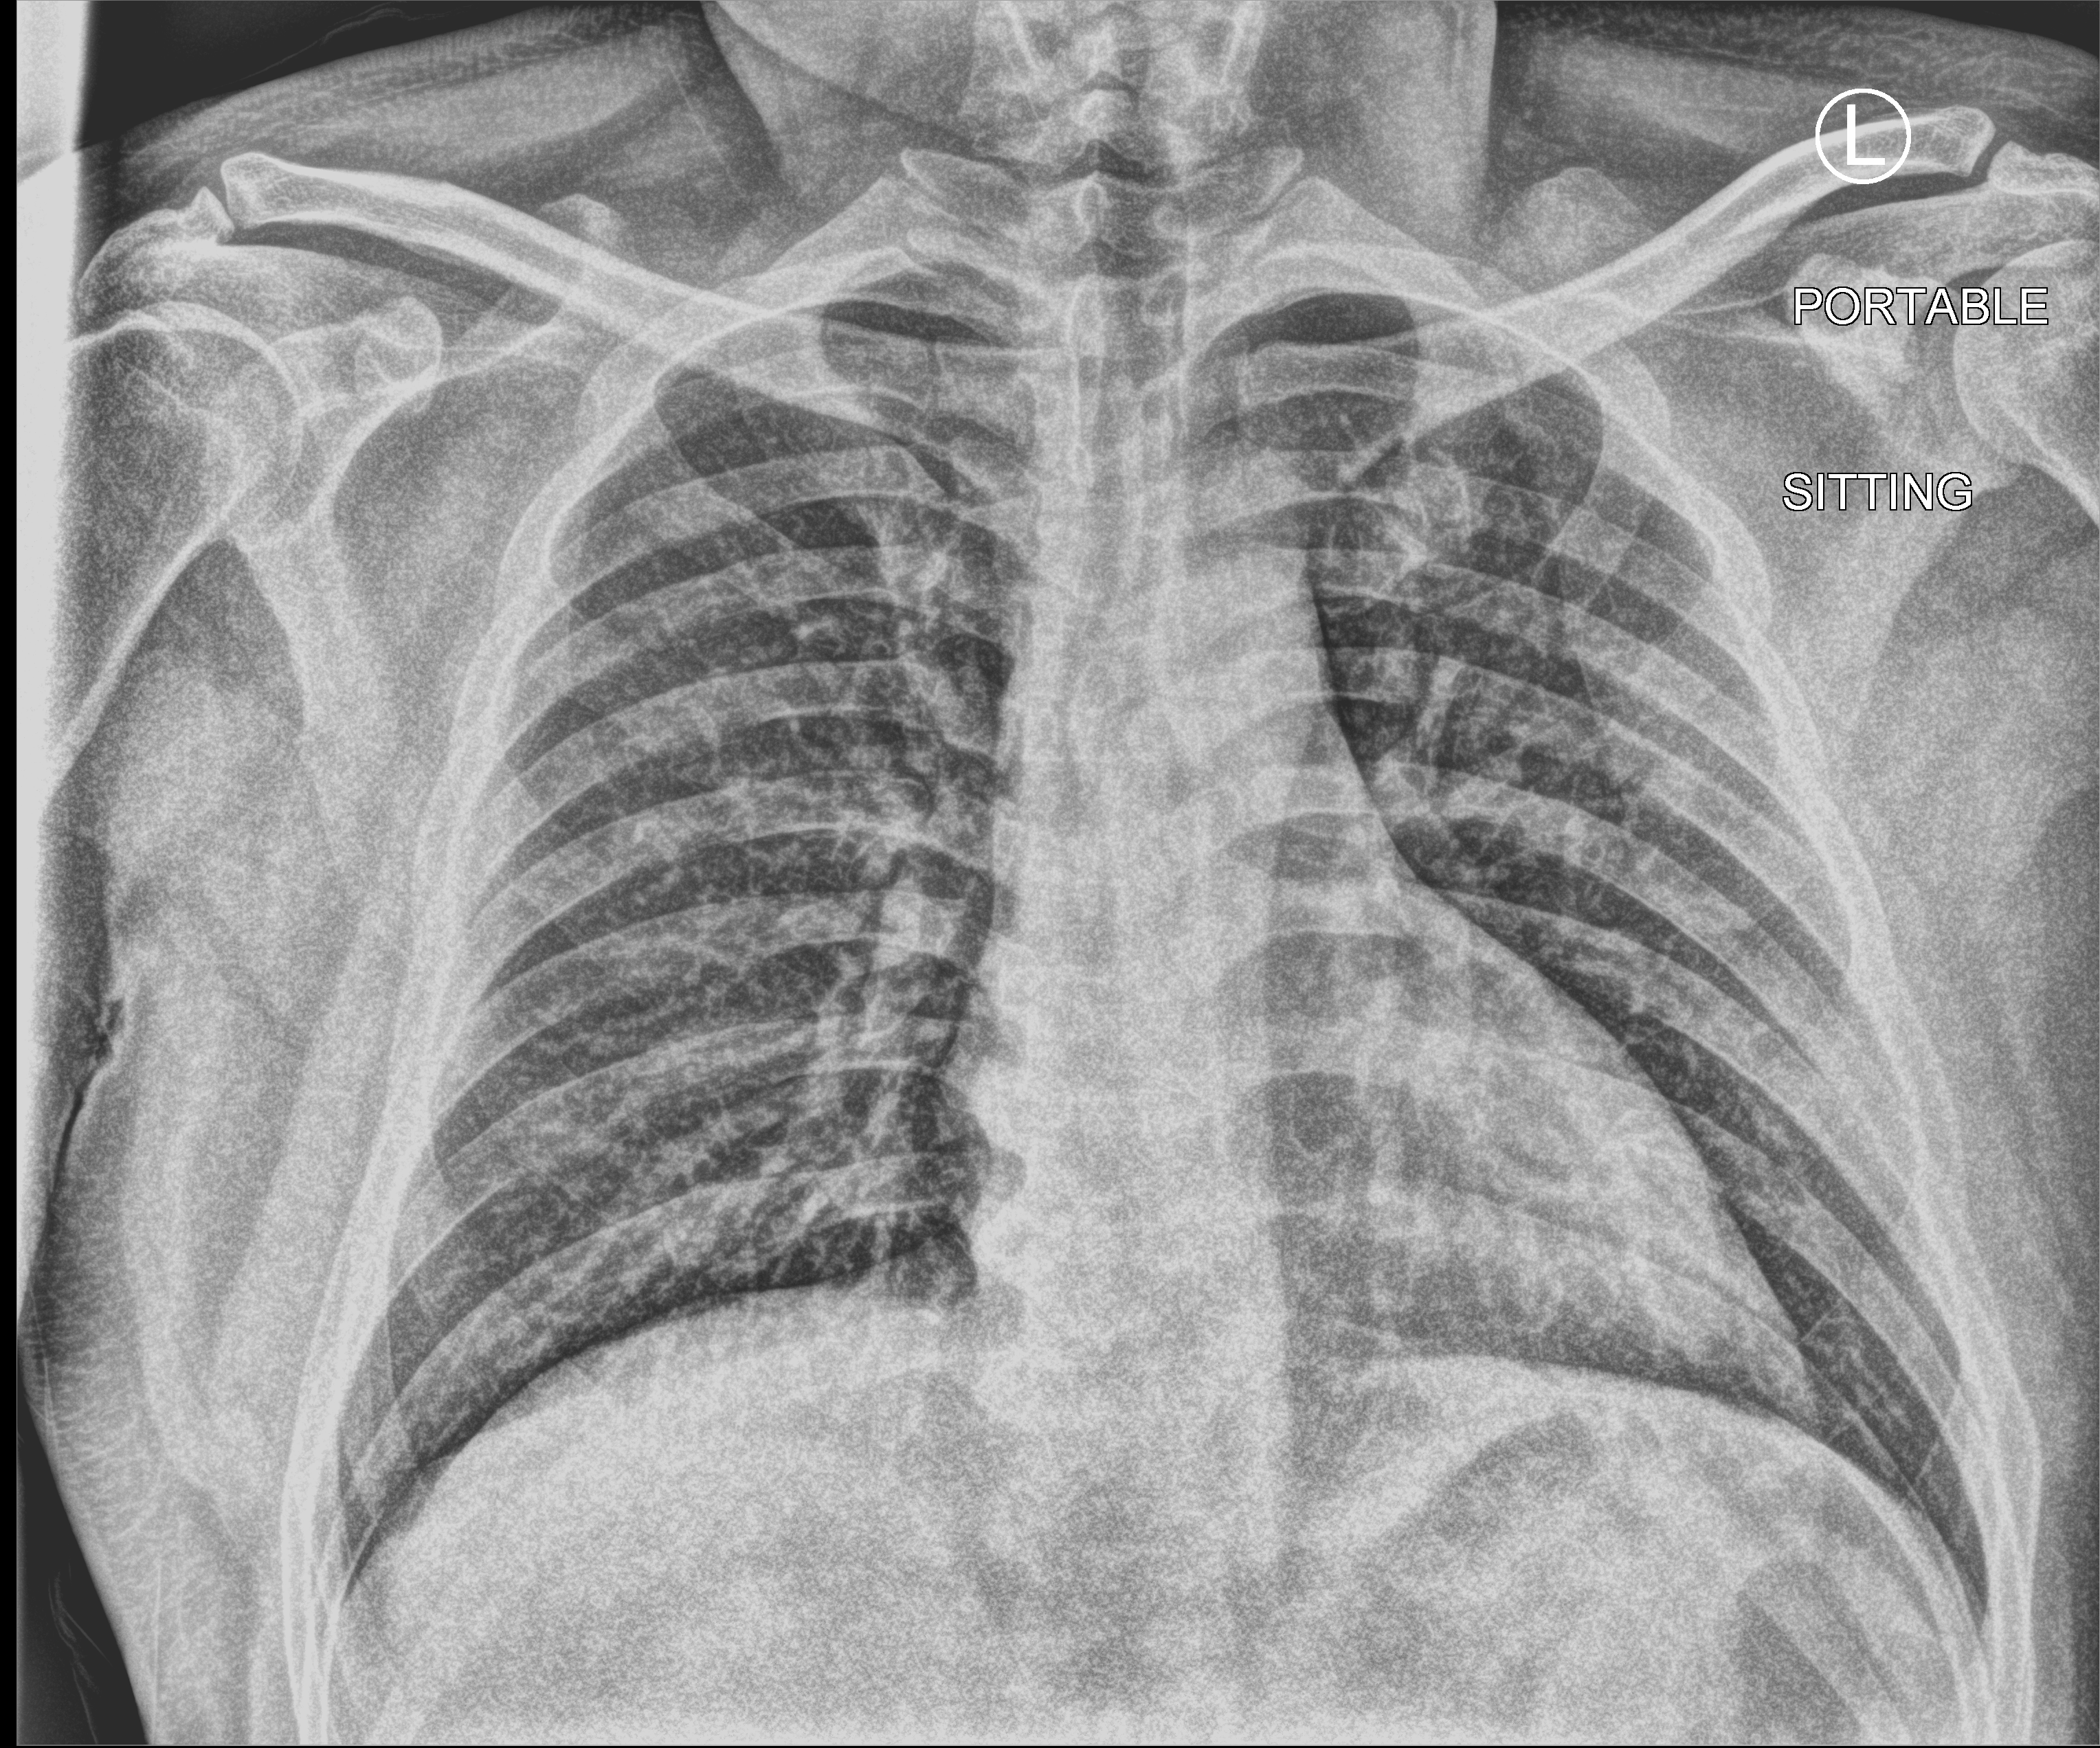
Portable chest radiograph; anteroposterior (AP) projection. Patient hospitalised with COVID-19; male, aged 18–59 years.
Admission-level facts for this patient (not findings on this image; timing relative to this image not recorded): admitted to intensive care during this hospital stay: no.